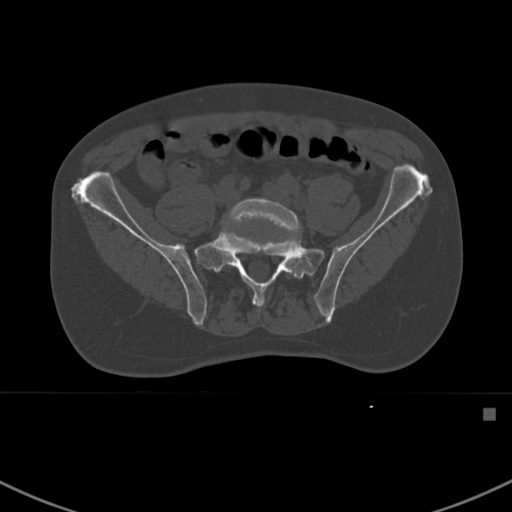
CT including the spine, one axial slice; position 207 of 412 along the scan axis; bone window (W 1800 / L 400 HU); 1.5 mm slice thickness; 512 × 512 image matrix. Patient: male, 59 years. From the clinical record (not read from this slice): primary cancer: prostate.
Annotated regions visible in this slice (semi-automatically segmented with operator editing):
- L5 vertebra: bounding box [x1, y1, x2, y2] px = [225, 199, 300, 234]